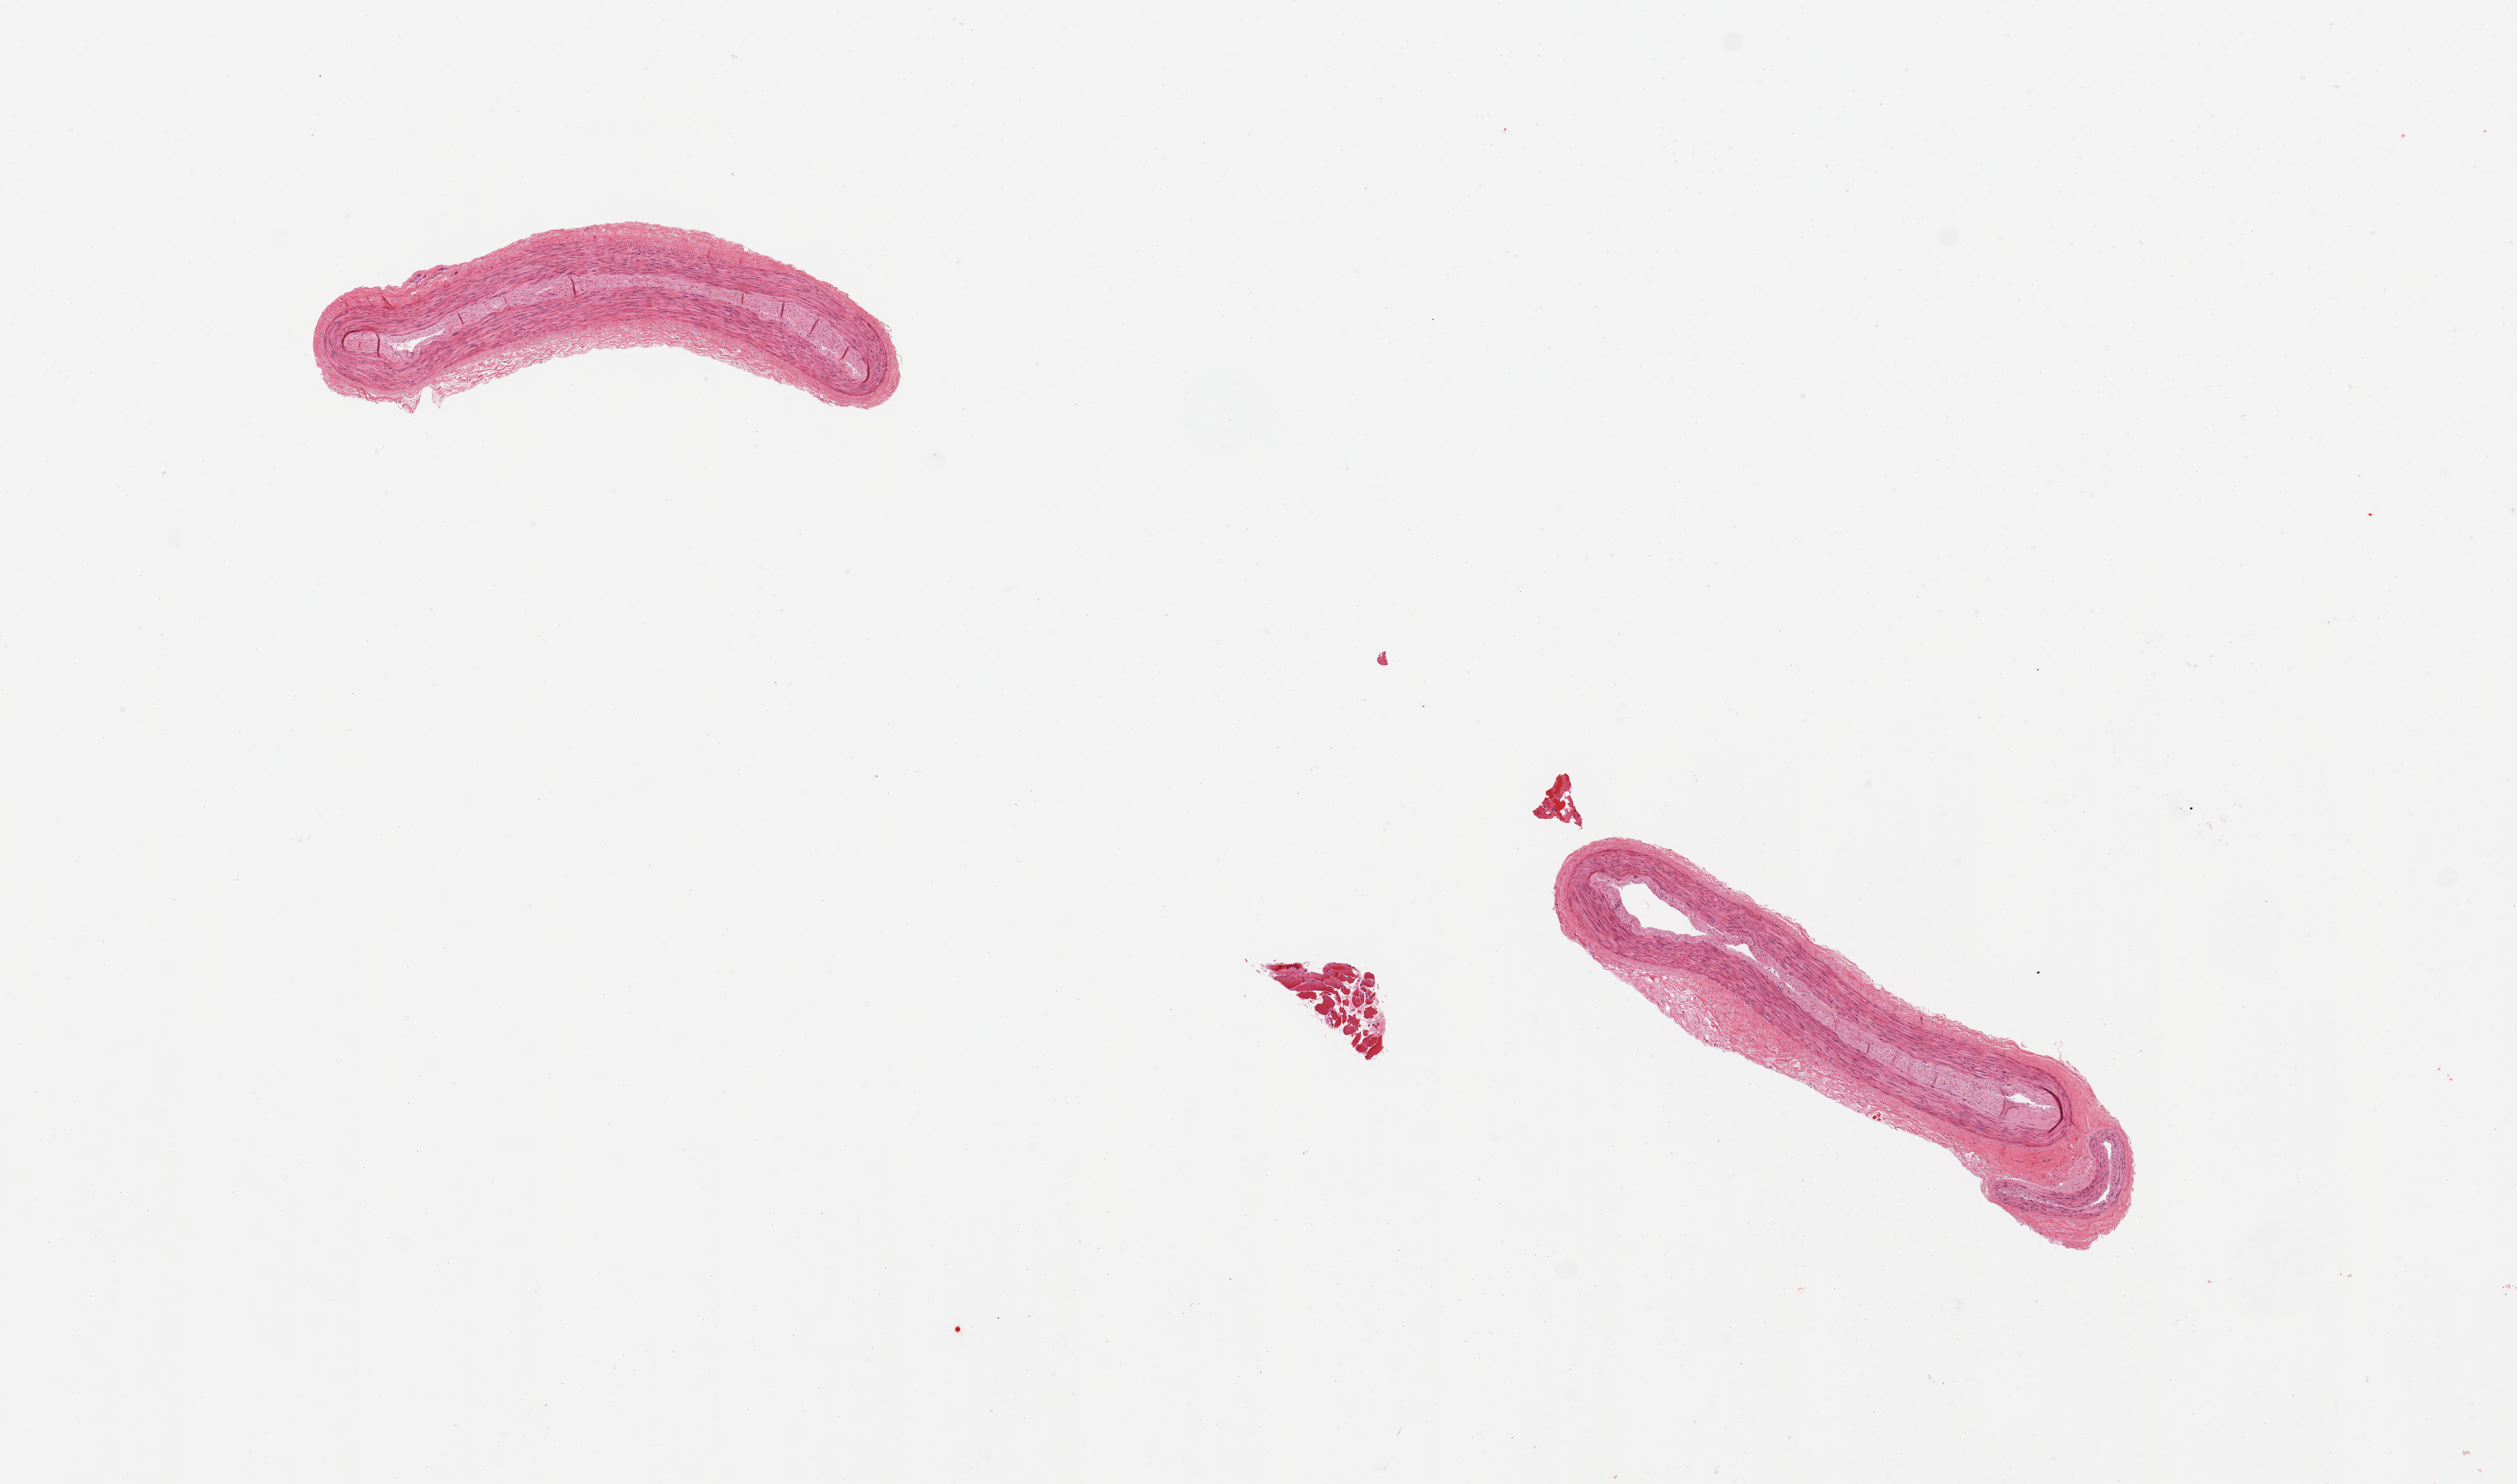
Haematoxylin and eosin whole-slide image — a low-resolution overview of the entire scanned area, about 13.8 x 8.1 mm (acquisition: 20x scan); PAXgene-fixed paraffin-embedded (PFPE) section; target tissue: tibial artery; donor tissue sample. Donor: female.
Review note (as recorded): 2 pieces; no plaques; well trimmed.